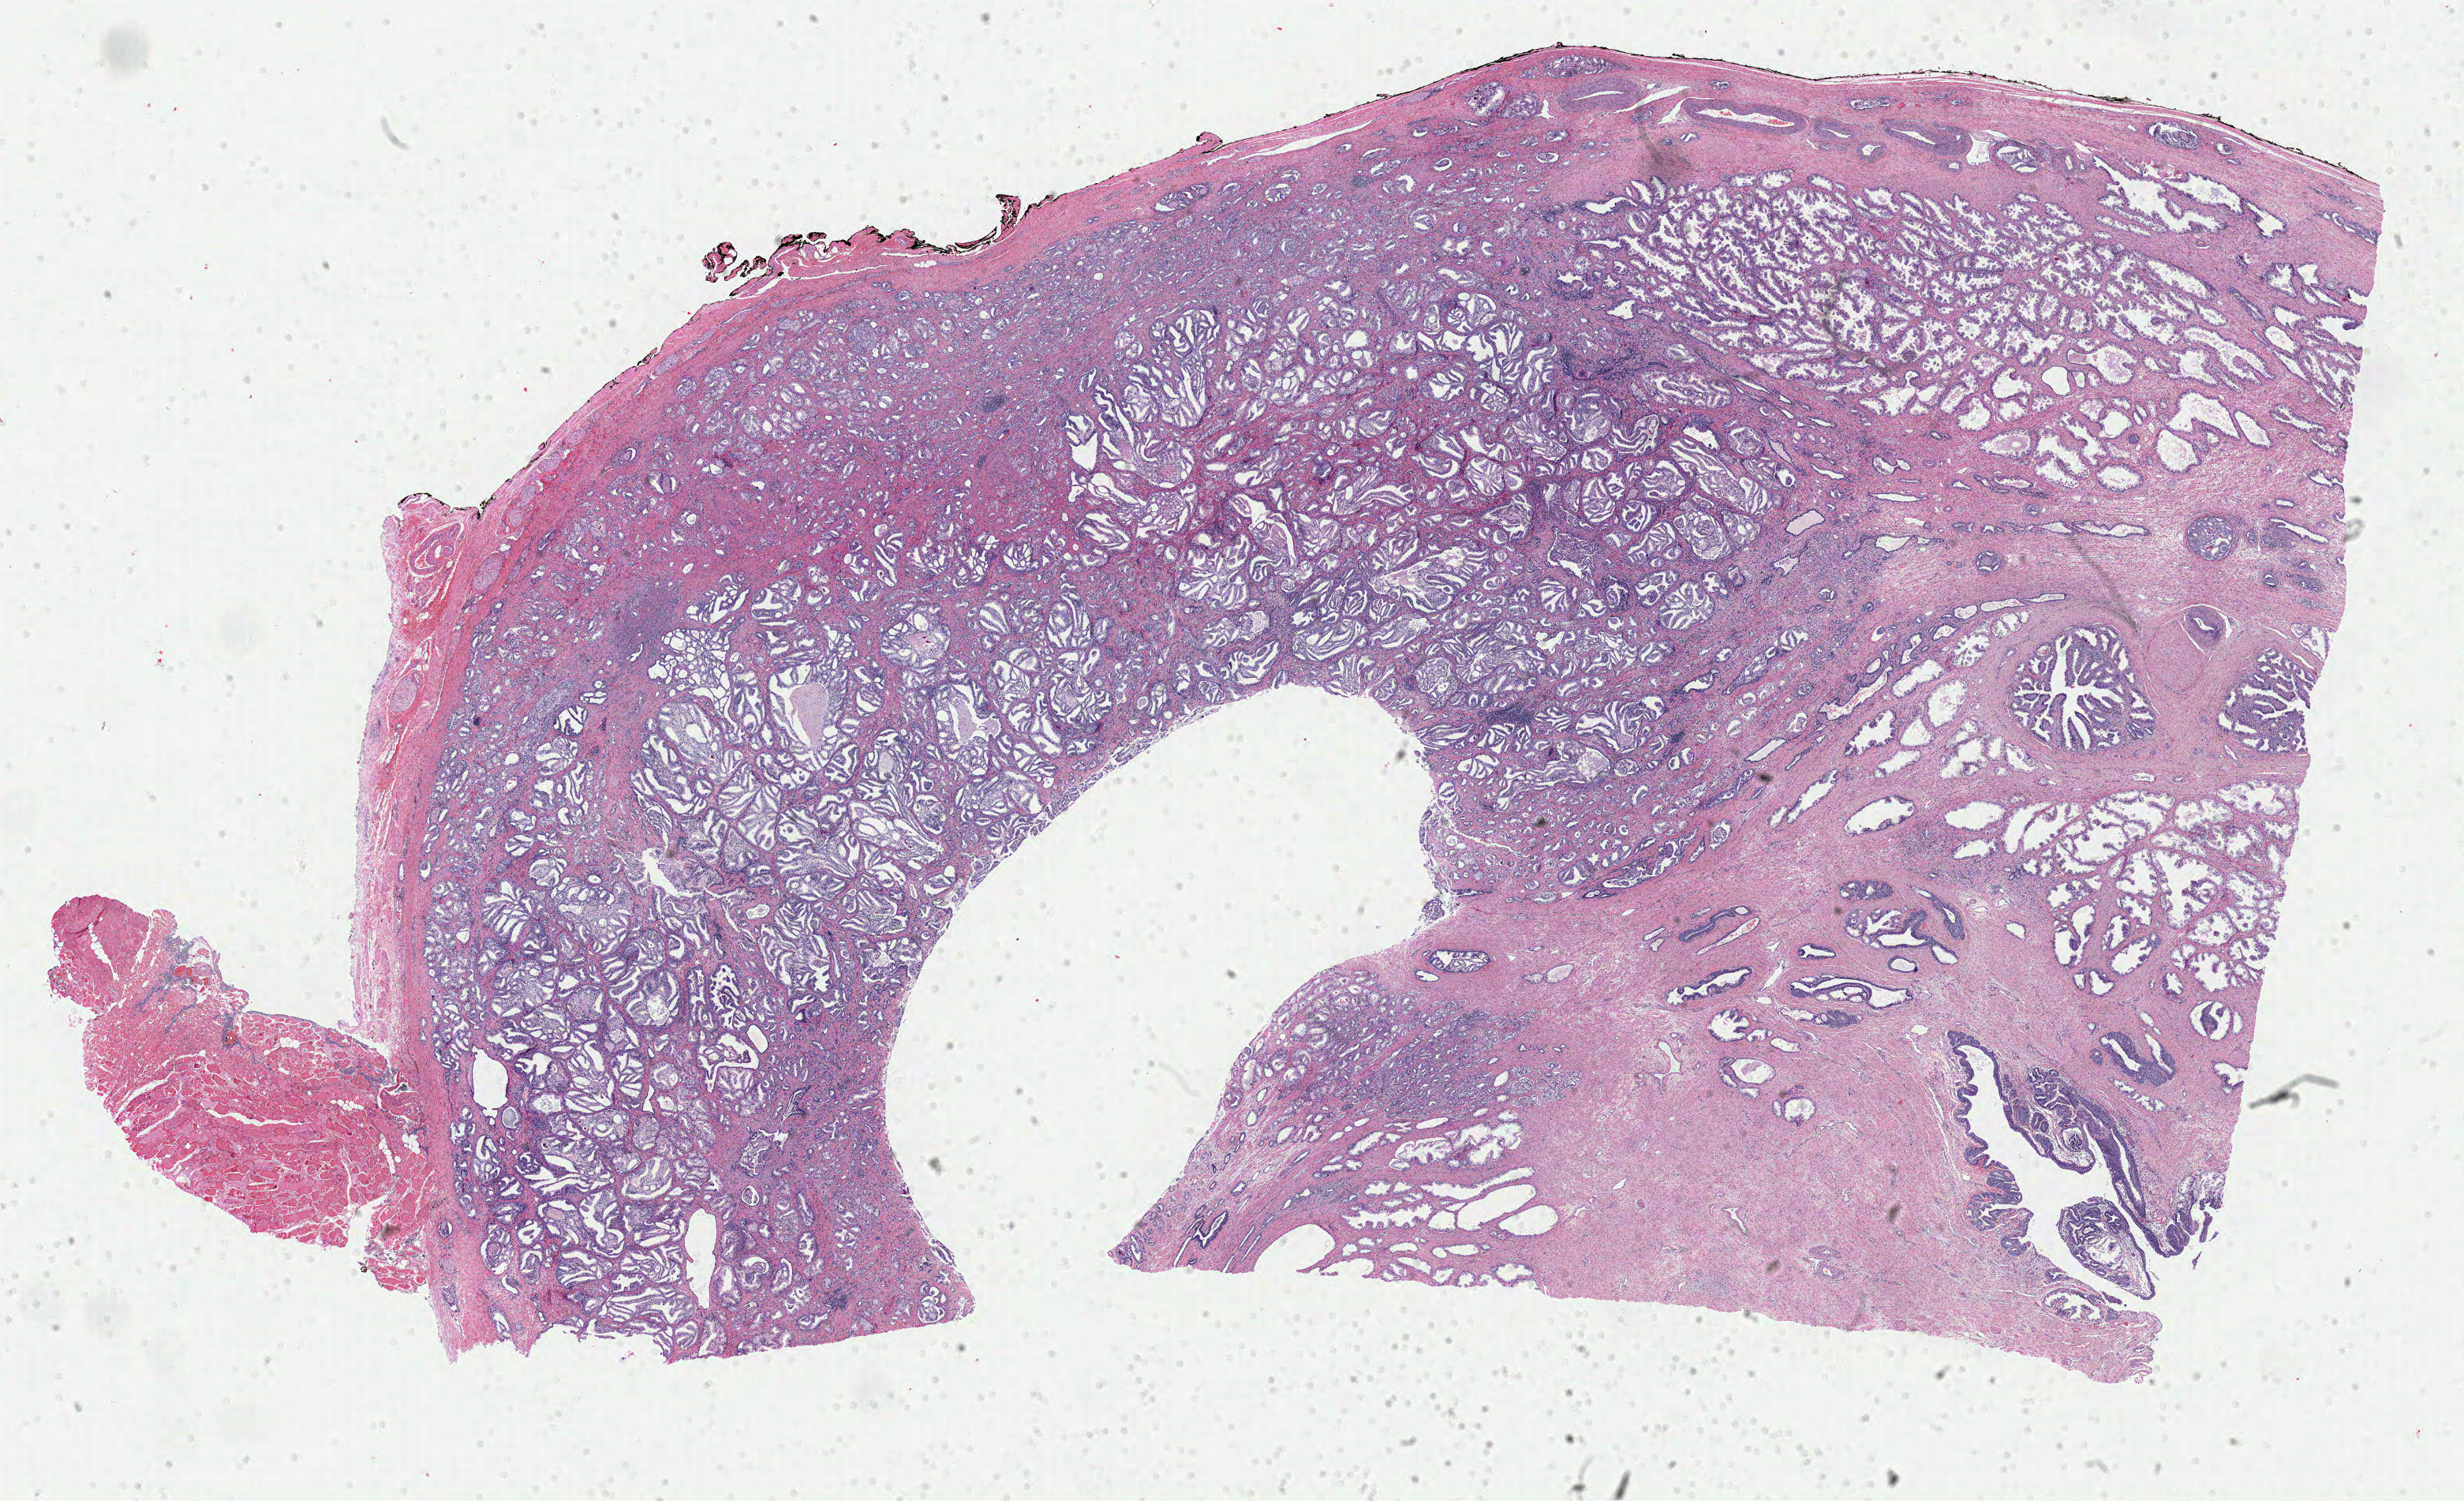
Hematoxylin and eosin (H&E) stained whole-slide image, shown as a low-resolution overview of the whole scanned area (about 24.7 x 15.0 mm, slide scanned at 40x), FFPE section, prostate, primary tumour sample. Male, age 56 years at initial diagnosis. Gleason score: 9 (4+5).
Diagnosis: Adenocarcinoma, NOS. Laterality: bilateral. Lymph nodes positive (case pathology): 2 of 4 examined.